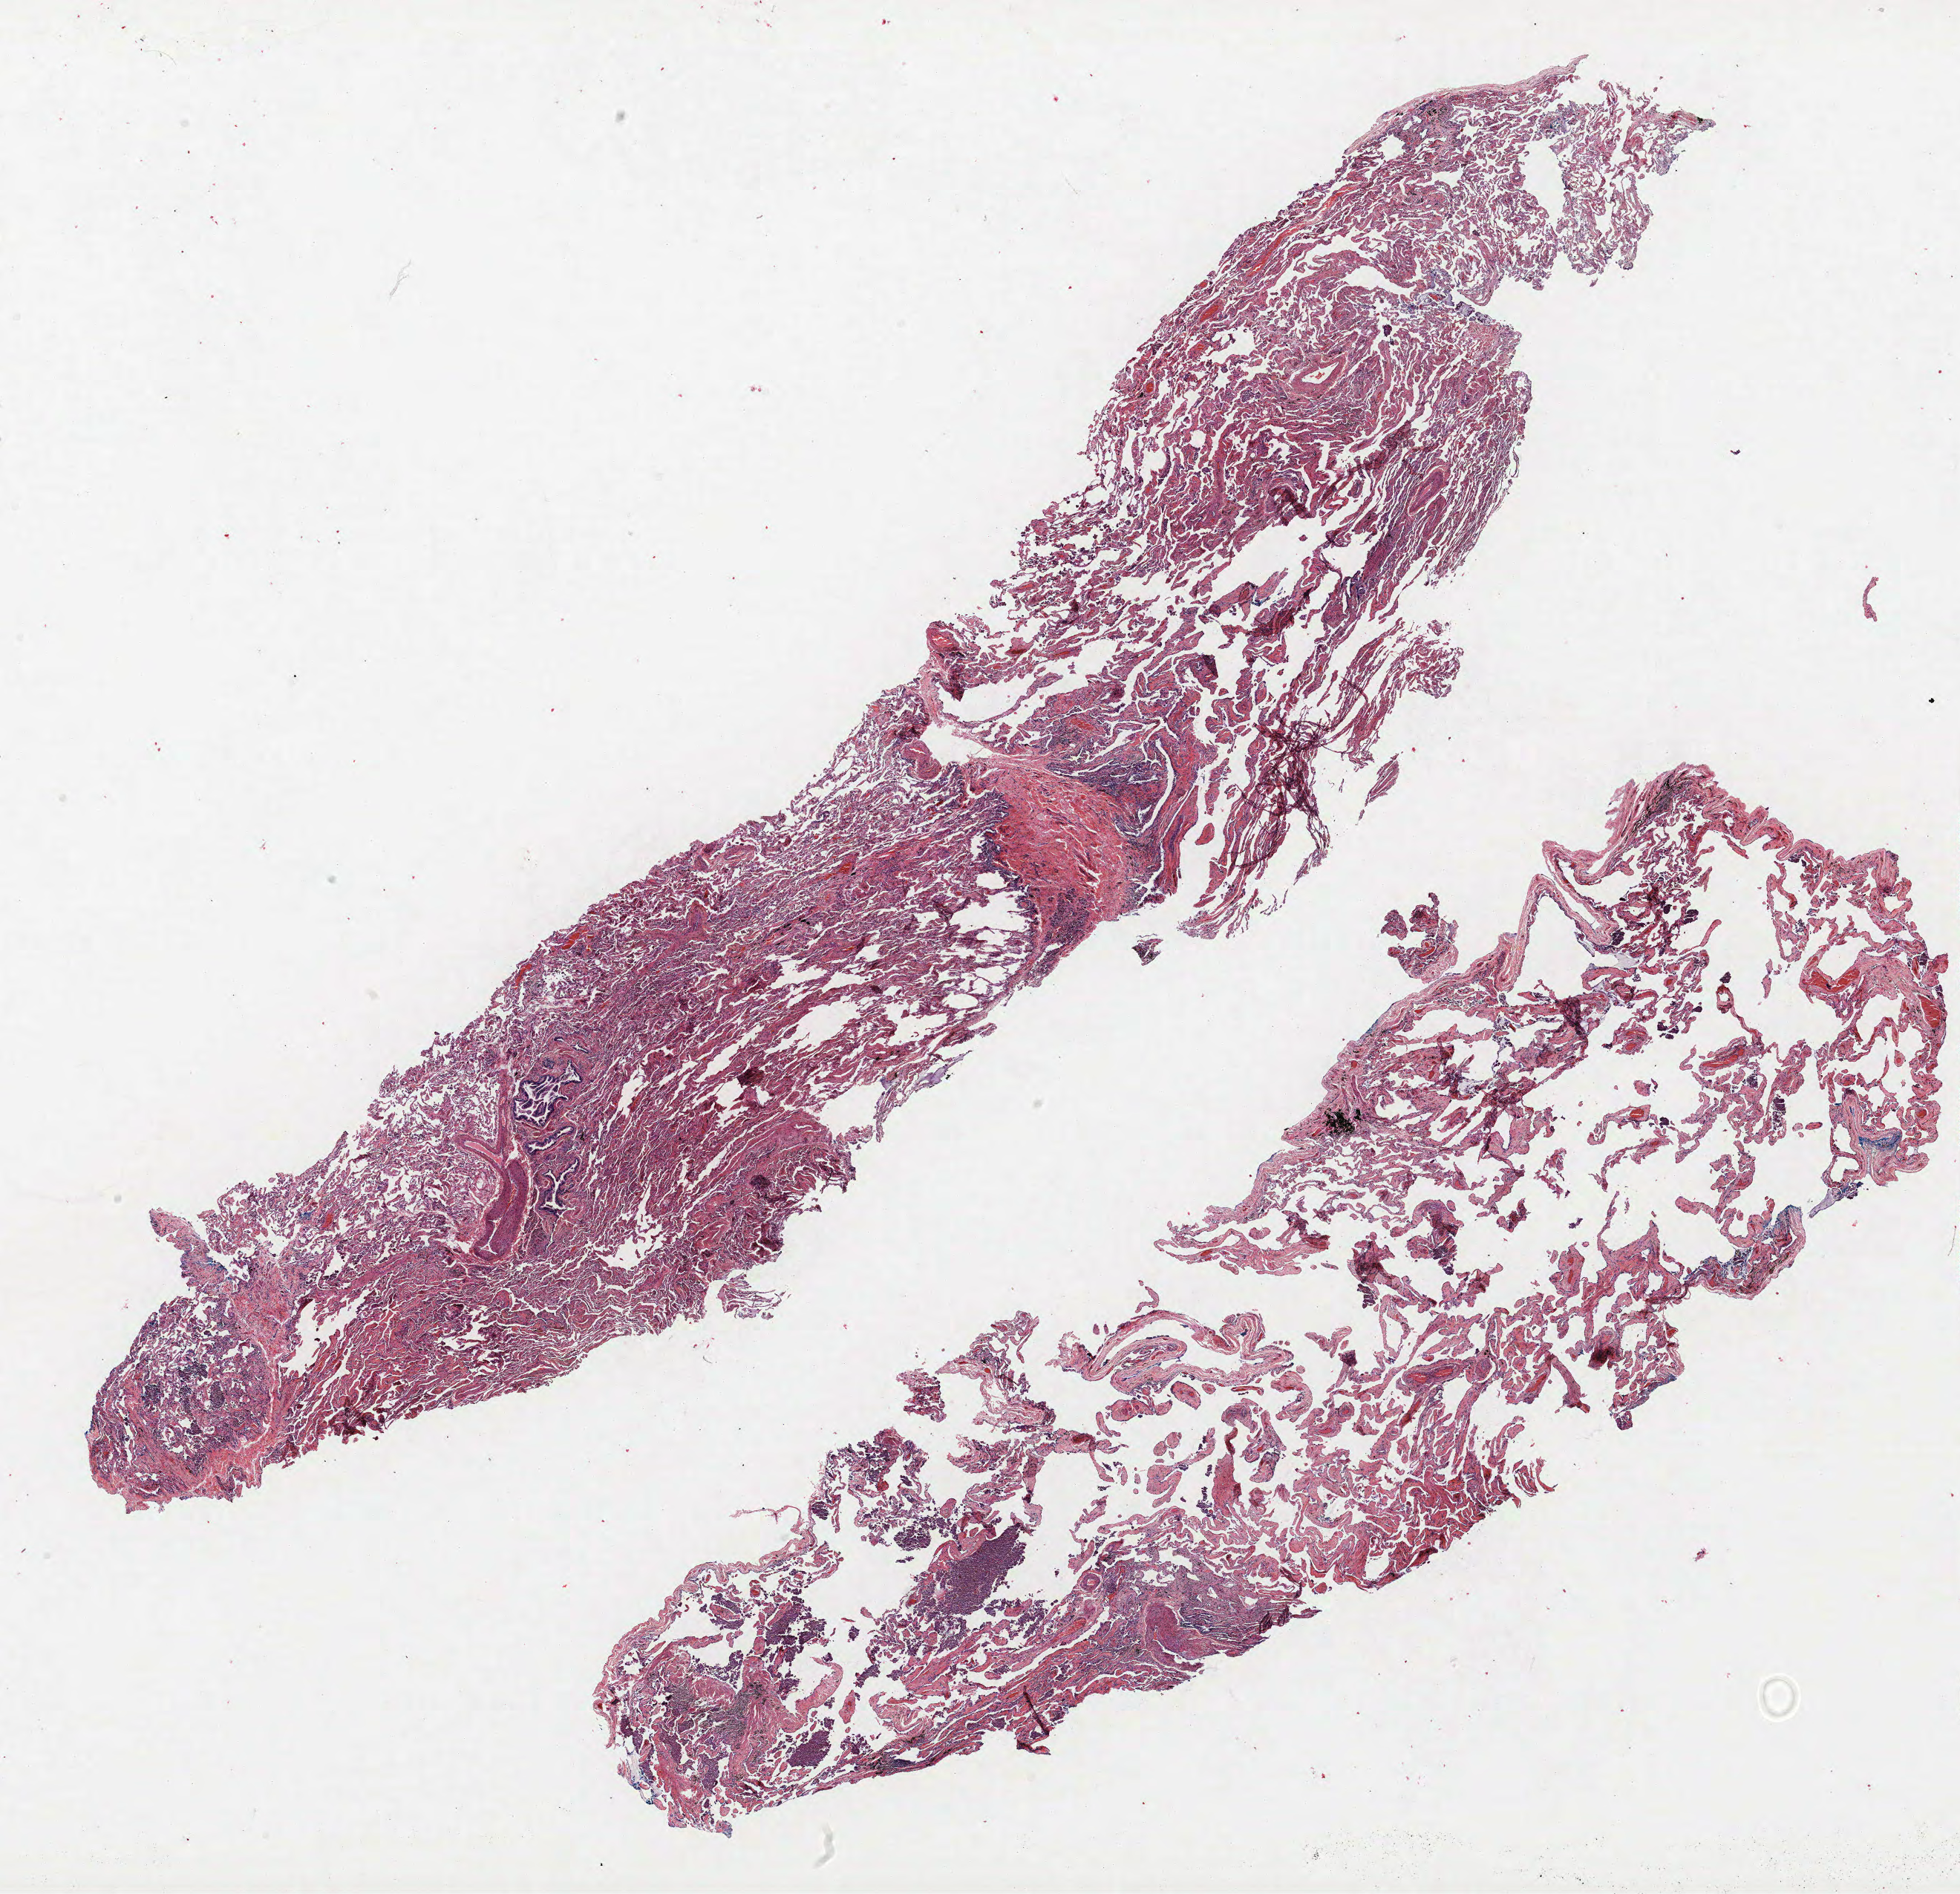
H&E-stained whole-slide image — low-resolution overview of the scanned area, about 21.1 x 20.4 mm, FFPE section, lung tissue. Male patient, aged 66 at enrolment. Current smoker at enrolment. Grade: well differentiated (G1).
Participant's lung-cancer diagnosis: Bronchiolo-alveolar carcinoma, mucinous. Tumour size (pathology): 18 mm. ICD-O-3 topography: upper lobe of lung (C34.1). Primary tumour location (clinical record): left upper lobe. Stage (AJCC 6th edition): IA.